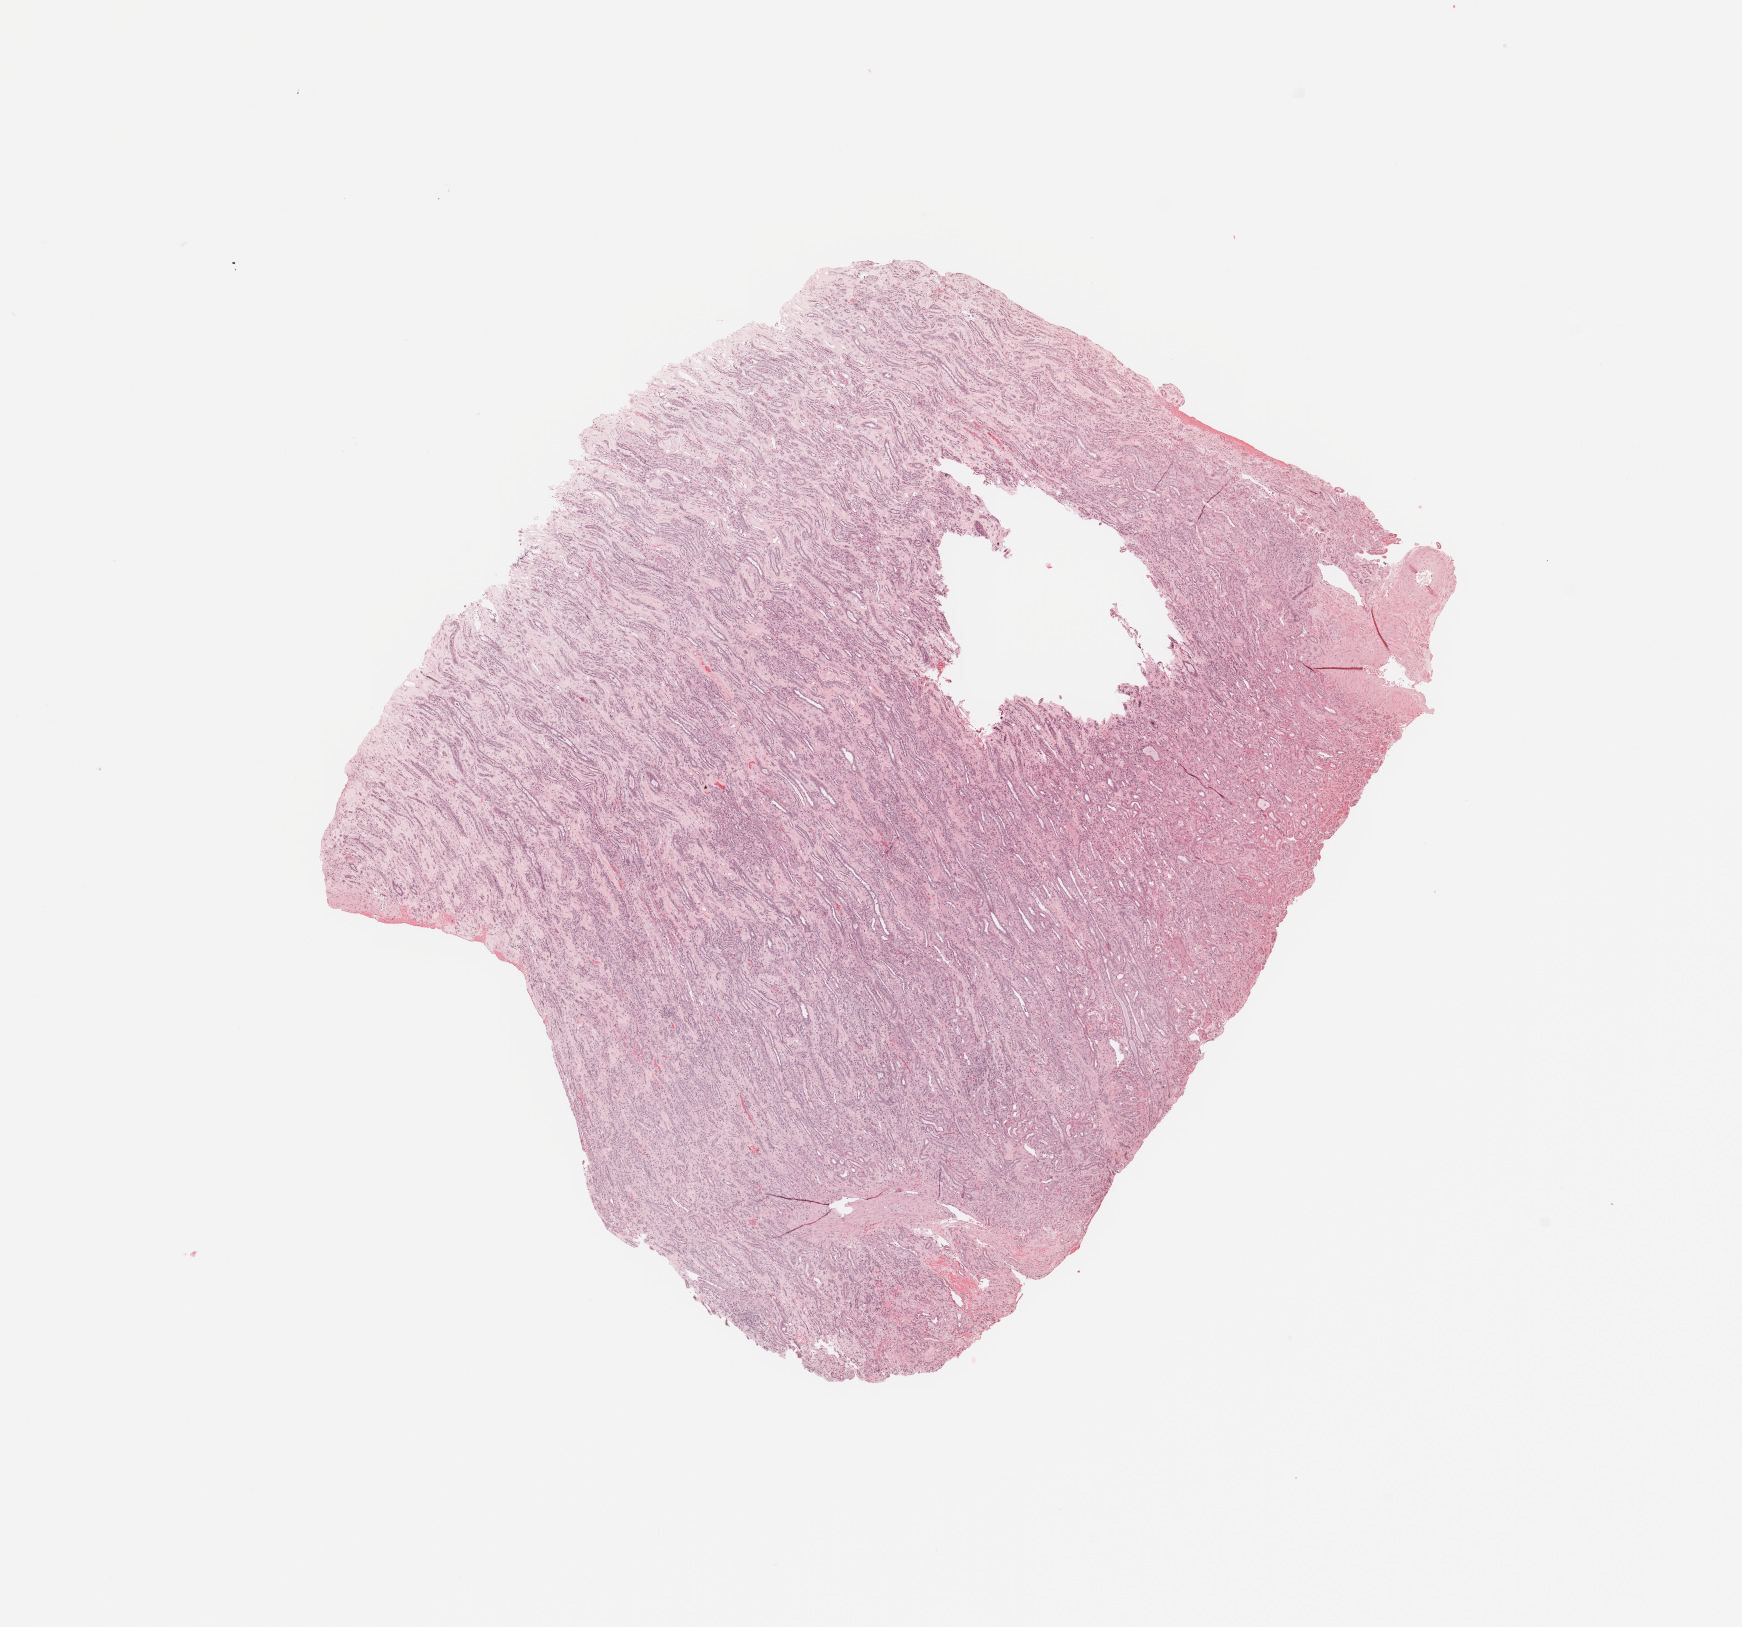
Whole-slide histology image, H&E, low-resolution overview of the scanned area, about 13.8 x 12.9 mm; normal (non-tumour) tissue sample, sampled site: kidney. Patient: male, age 68 years.
- this section: normal (non-tumour) tissue from the same patient
- patient diagnosis: Renal cell carcinoma, NOS